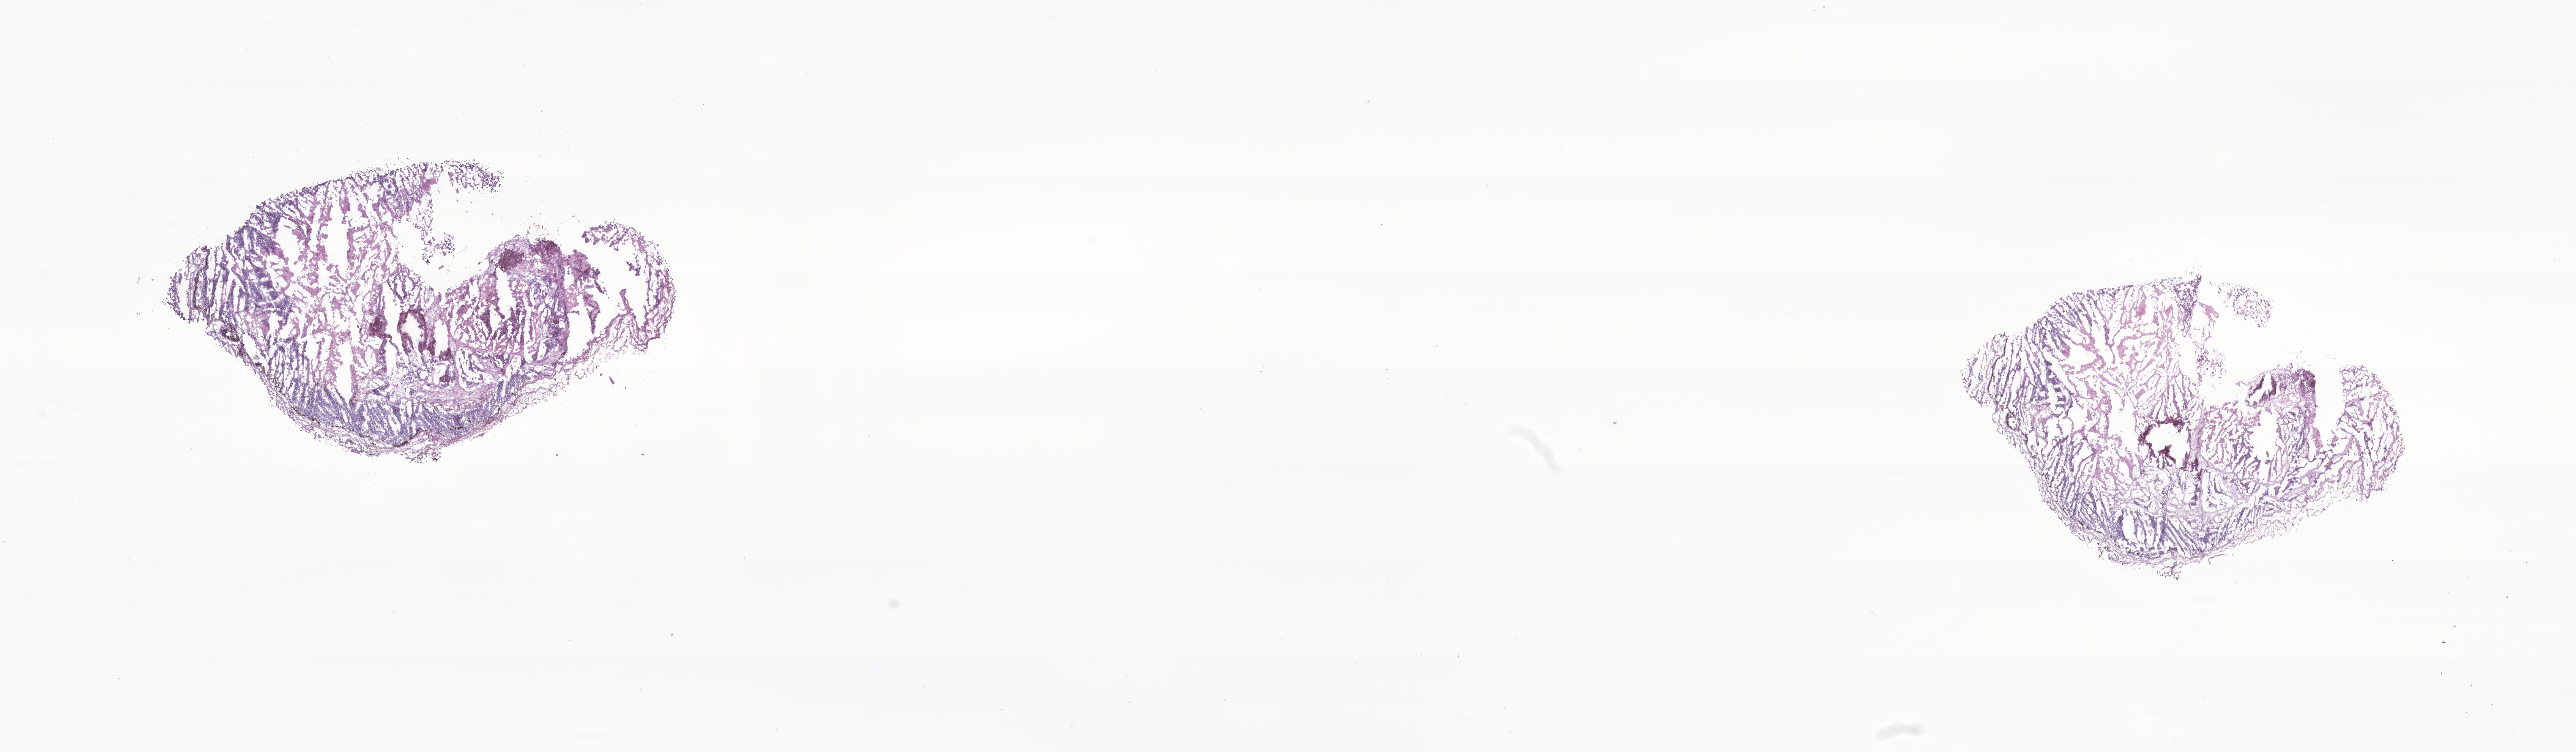
Digitized hematoxylin and eosin (H&E)-stained section of tumor tissue from the eye — a low-resolution overview of the entire scanned area, about 28.6 x 8.4 mm, frozen section (OCT-embedded). Patient male; age 733 days (about 2.0 years).
Diagnosis (ICD-O-3 morphology term): Retinoblastoma, NOS.